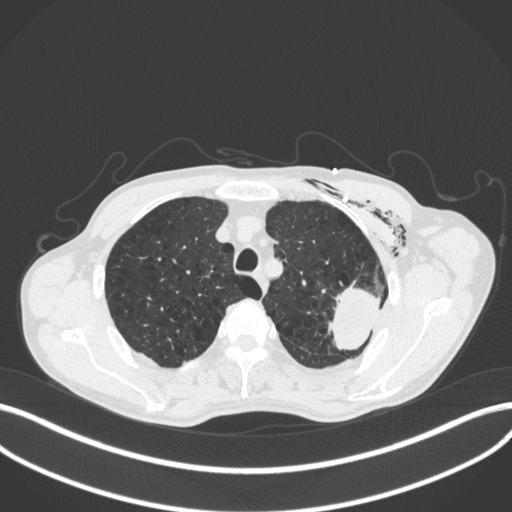
Chest CT, one axial slice. Slice 329 of 416 in the series (ordered by position). Reconstruction kernel B31f. 120 kVp. Lung window (W 1500 / L -600 HU). 1 mm slice thickness. 512 × 512 image matrix, field of view 400 × 400 mm. Patient: male, 58 years. From the clinical record (not read from this slice): clinical TNM (as recorded): T3 N0 M0.
Outlined on this slice (bounding box drawn by a radiologist):
- lung tumour (recorded histology: adenocarcinoma): bounding box (x1, y1, x2, y2) in pixels: (319, 278, 384, 354)